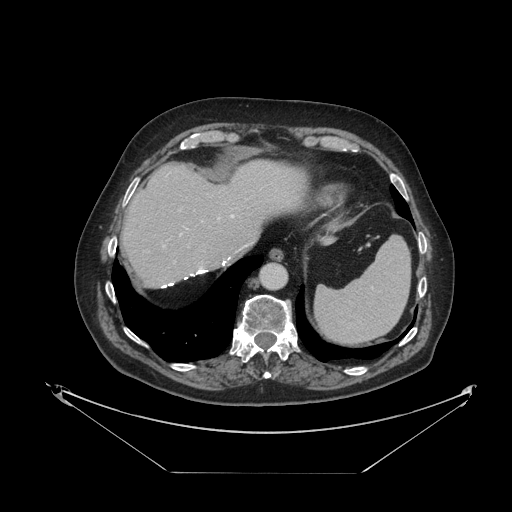
Contrast-enhanced abdominal CT, one axial slice; soft-tissue window (W 400 / L 40 HU); 512 × 512 image matrix, field of view 500 × 500 mm. Male patient, age 68 years. From the clinical record (not read from this slice): diagnosis: colorectal cancer liver metastases, imaged before liver resection; multiple liver metastases: no; largest metastasis: 4 cm; disease in both lobes: no.
Structures marked on this image (manually delineated by an expert):
- hepatic veins: bounding box [x1, y1, x2, y2] px = [181, 215, 234, 235]
- liver: [123, 160, 306, 287]
- planned liver remnant (the part of the liver to remain after resection): [123, 160, 305, 287]
- portal vein (with intrahepatic branches): [163, 217, 220, 263]